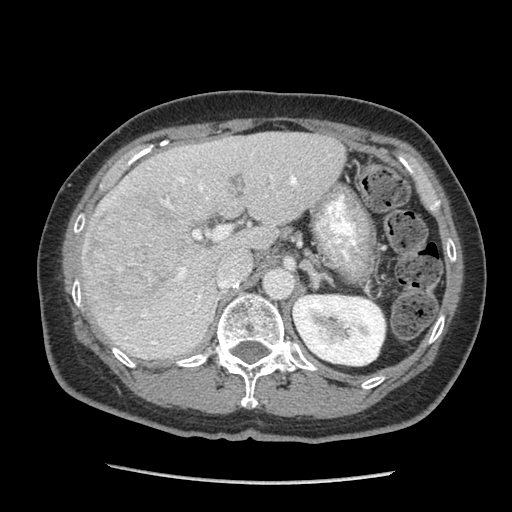
Contrast-enhanced abdominal CT (liver protocol), one axial slice; position 52 of 105 along the scan axis; 140 kVp; soft-tissue window (W 400 / L 40 HU); 2.5 mm slice thickness; 512 × 512 image matrix, field of view 340 × 340 mm. Case-level facts recorded for this patient, not image findings: diagnosis: hepatocellular carcinoma (patient treated with transarterial chemoembolisation; whether this scan precedes or follows treatment is not stated here); TNM stage (as recorded): Stage-I; Child-Pugh class: A; tumour differentiation: moderately differentiated; tumour size: 11.1 cm.
Structures marked on this image (semi-automatic segmentation, software-assisted and operator-edited):
- liver parenchyma outside the tumour (the mass and vessels are separate outlines, so this box may not span the whole liver): bounding box <80,132,344,359> (left, top, right, bottom; pixels)
- mass: <84,197,193,304>
- liver vessels: <113,170,297,351>